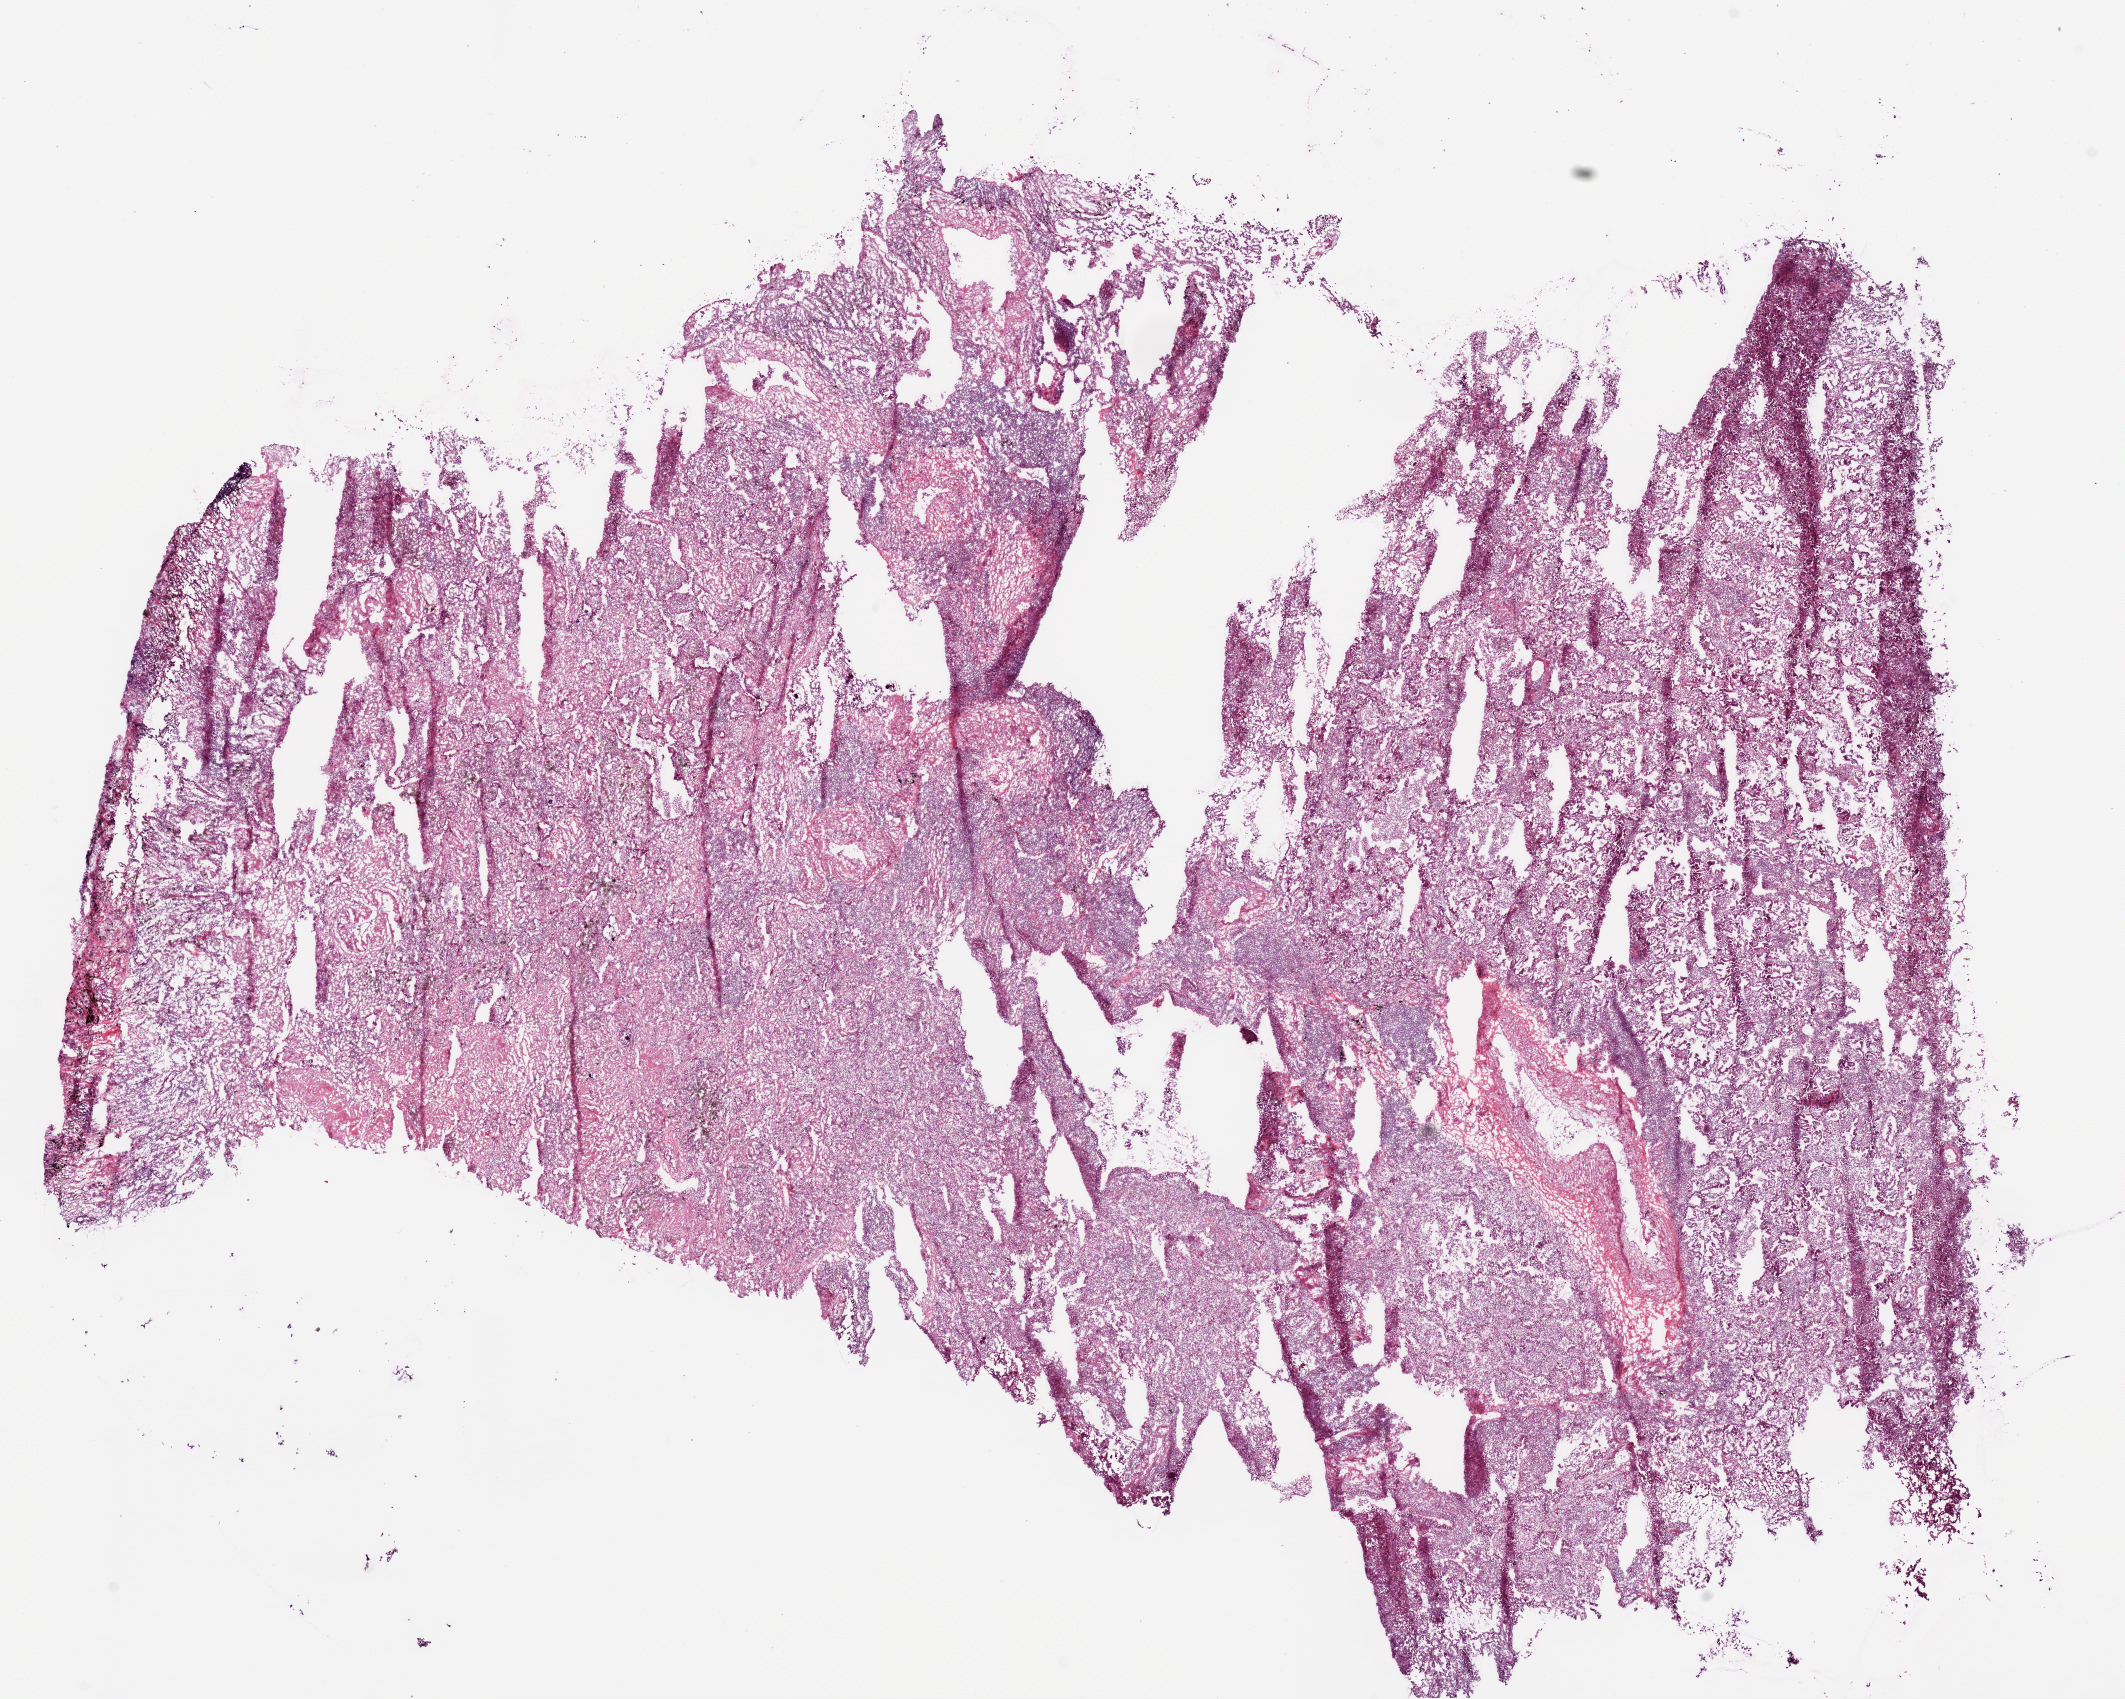
Whole-slide histology image, H&E-stained — shown as a low-resolution overview of the whole scanned area (about 17.1 x 13.6 mm, slide scanned at 20x). Frozen section from the bottom of the tissue portion. Lung, primary tumour sample. Female patient; age at initial diagnosis 59 years.
Diagnosis: Adenocarcinoma, NOS (lower lobe, lung).